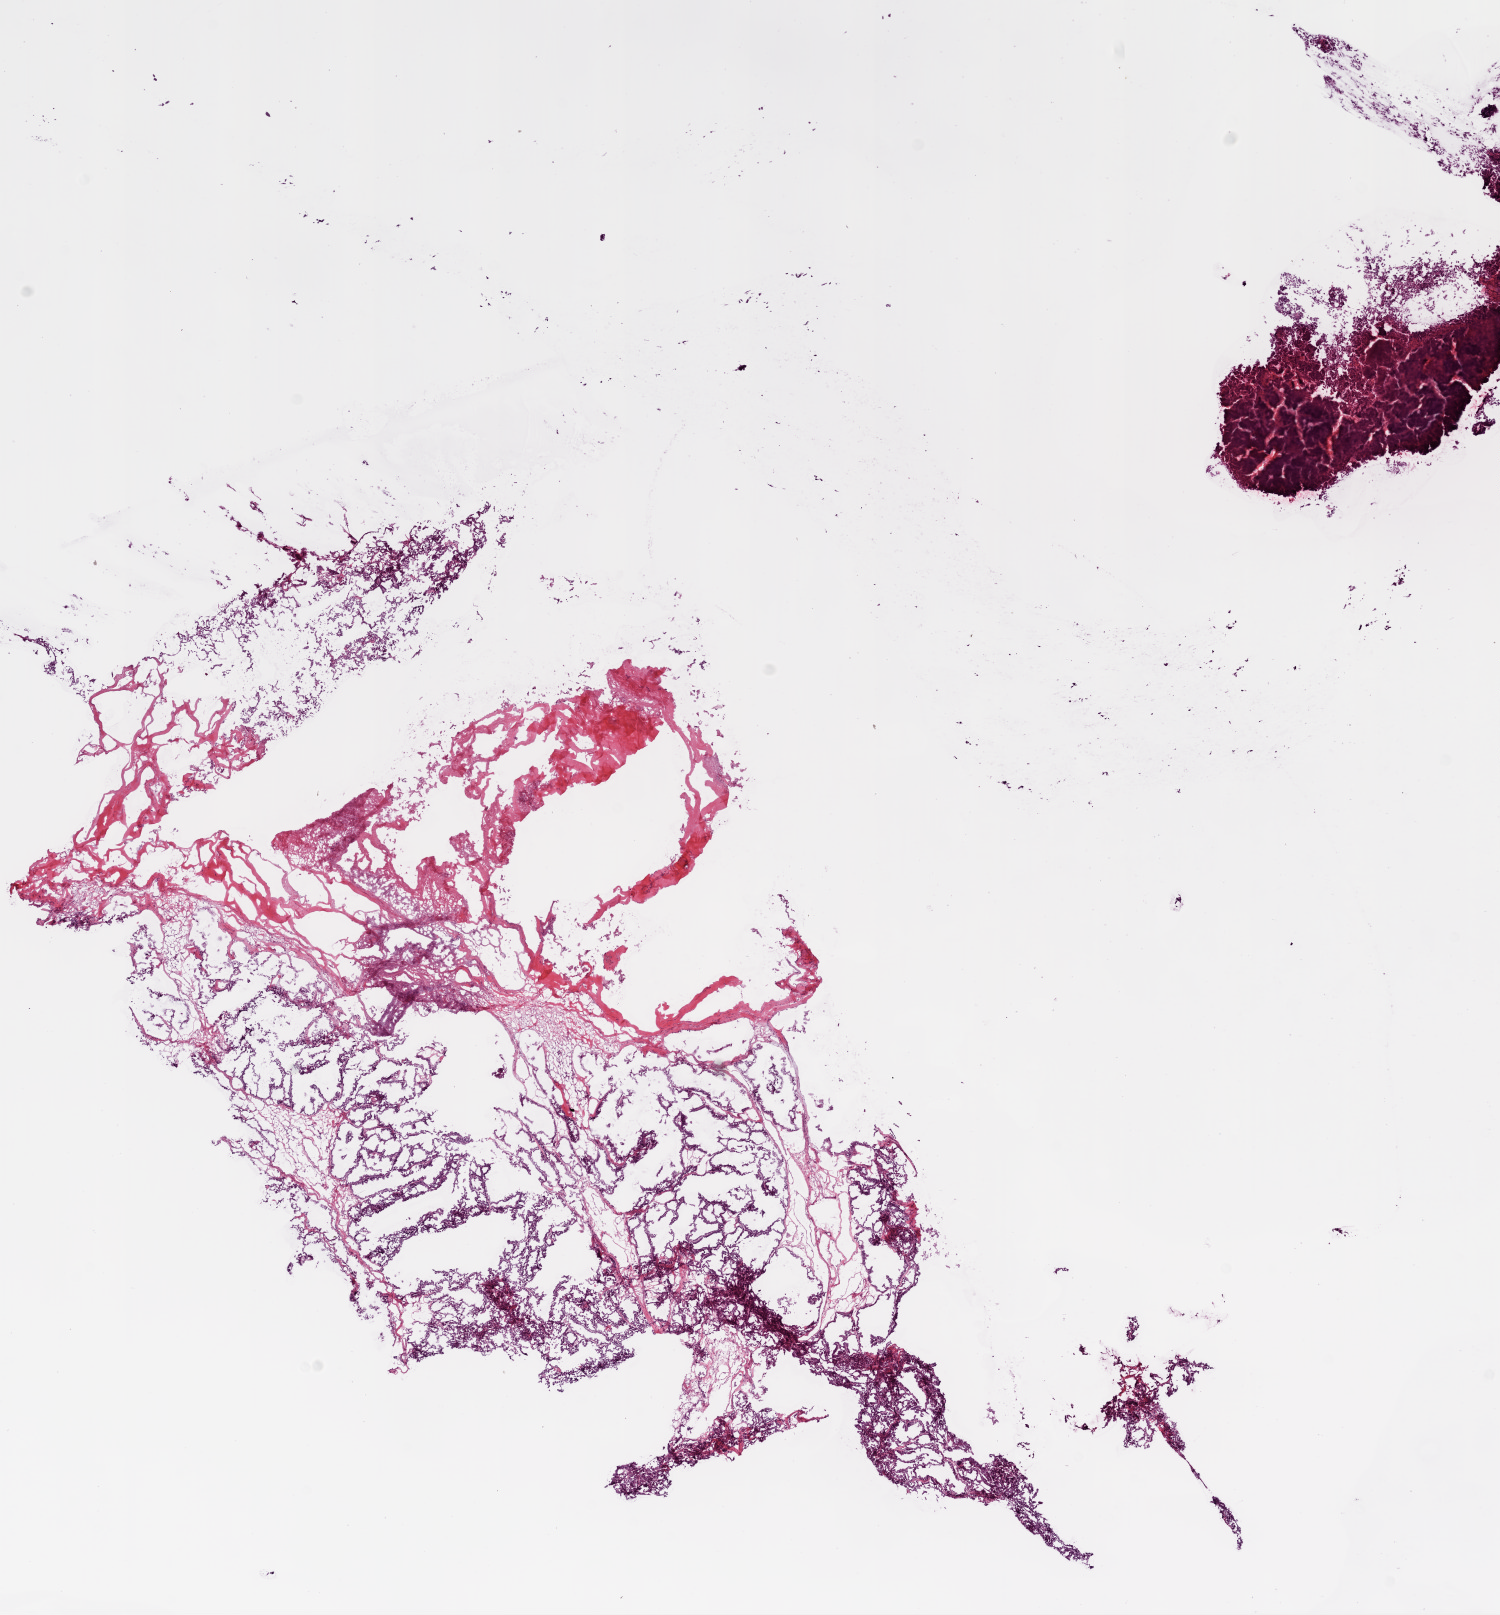
Whole-slide histology image, H&E-stained — a low-resolution overview of the entire scanned area, about 12.0 x 13.0 mm (slide scanned at 20x). Frozen section from the bottom of the tissue portion. Sample: primary tumour, ovary. Patient: female, age at initial diagnosis 57 years. Histologic grade: G2 (moderately differentiated). Pathologist review of this section (percent, as recorded): tumour cells 75%, tumour nuclei 80%, normal cells 0%, stromal cells 10%, necrosis 15%.
Pathologic diagnosis: Serous cystadenocarcinoma, NOS. FIGO stage: IIIC.